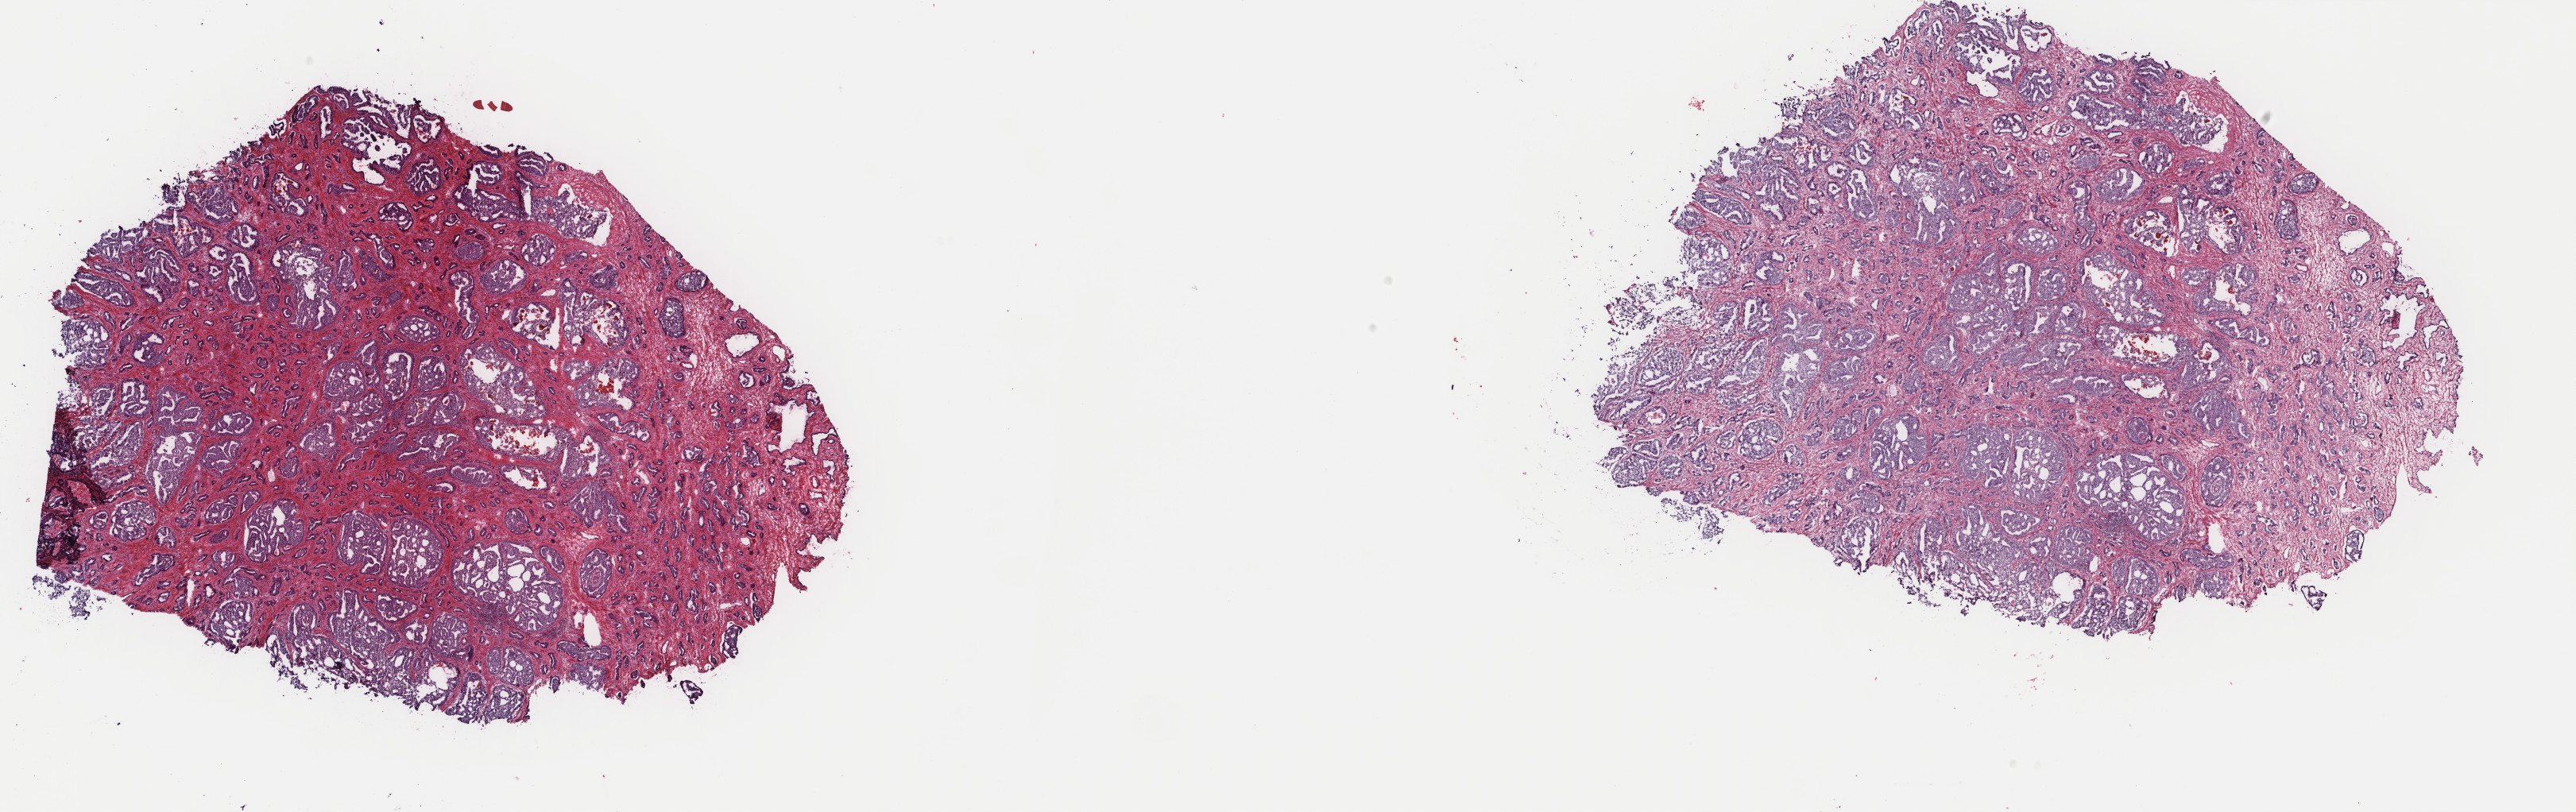
Digitized Hematoxylin and eosin (H&E) stained tissue section (whole slide), shown as a low-resolution overview of the whole scanned area (about 25.7 x 8.1 mm, acquisition: 40x scan), frozen section from the top of the tissue portion, primary tumour sample from the prostate. Male patient; age at initial diagnosis 62 years. Gleason score: 9 (4+5). Composition of this section per pathologist review: tumour cells 60%, tumour nuclei 85%, normal cells 0%, stromal cells 35%, necrosis 5%. Infiltration values recorded for this section: lymphocyte infiltration 7%, monocyte infiltration 0%, neutrophil infiltration 0%.
• histologic diagnosis: Adenocarcinoma, NOS (prostate gland)